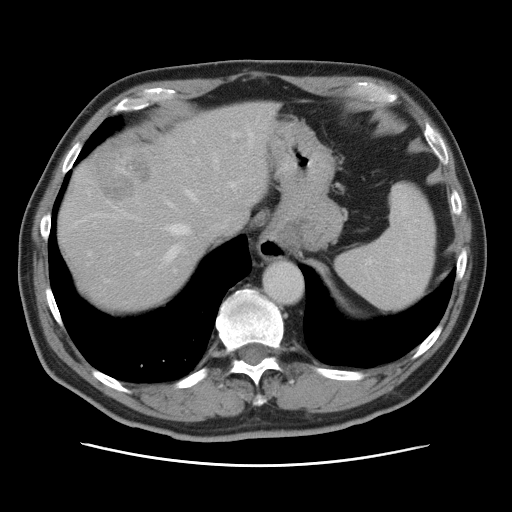
Contrast-enhanced abdominal CT, one axial slice. Soft-tissue window (W 400 / L 40 HU). 5 mm slice thickness. 512 × 512 image matrix. Male patient, age 69 years. From the clinical record (not read from this slice): diagnosis: colorectal cancer liver metastases, imaged before liver resection; multiple liver metastases: no; largest metastasis: 5 cm; chemotherapy before resection: no.
Structures marked on this image (outlined manually by an expert reader):
- hepatic veins: bounding box (x1, y1, x2, y2) in pixels: (89, 126, 256, 263)
- liver: (59, 101, 276, 313)
- planned liver remnant (the part of the liver to remain after resection): (59, 101, 276, 314)
- portal vein (with intrahepatic branches): (135, 130, 237, 271)
- liver metastasis: (92, 151, 151, 202)